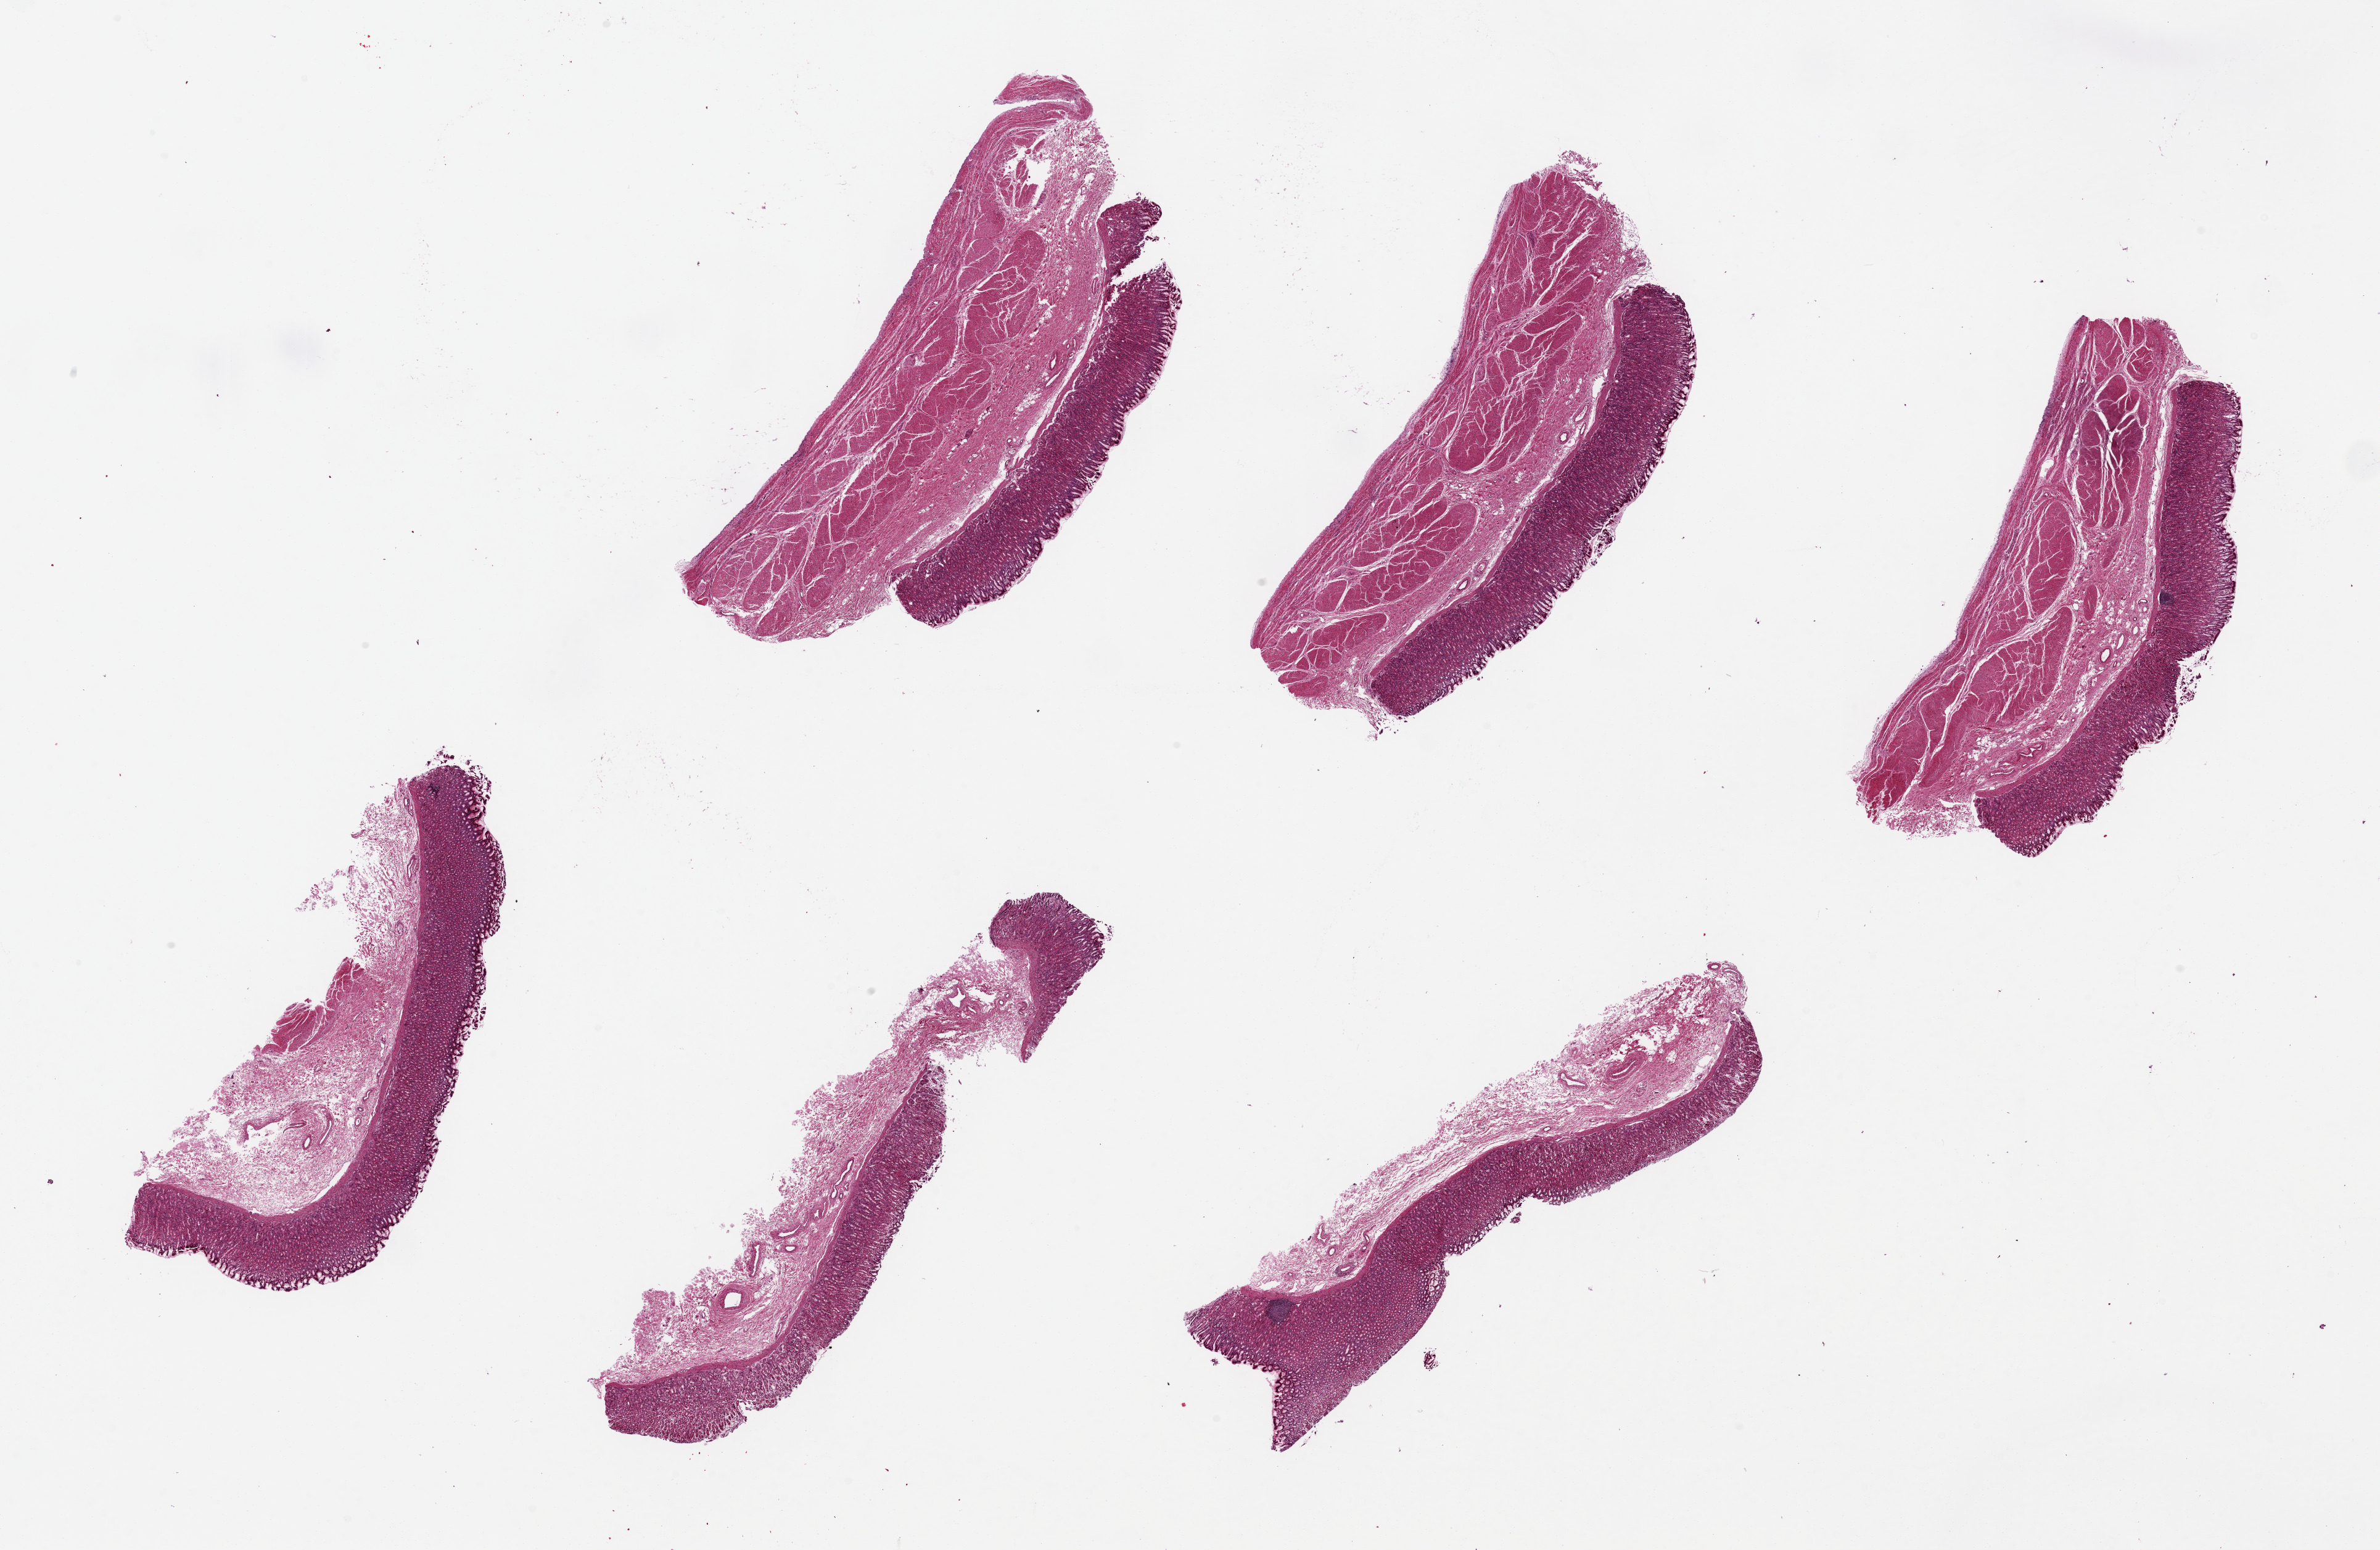
H&E whole-slide image, brightfield, low-resolution overview of the scanned area, about 30.5 x 19.9 mm, PAXgene-fixed paraffin-embedded (PFPE) section, target tissue: stomach, tissue donor sample. Female donor.
- review note (as recorded): 6 pieces, ~8x3mm mucosa well preserved, ~30-40% thickness